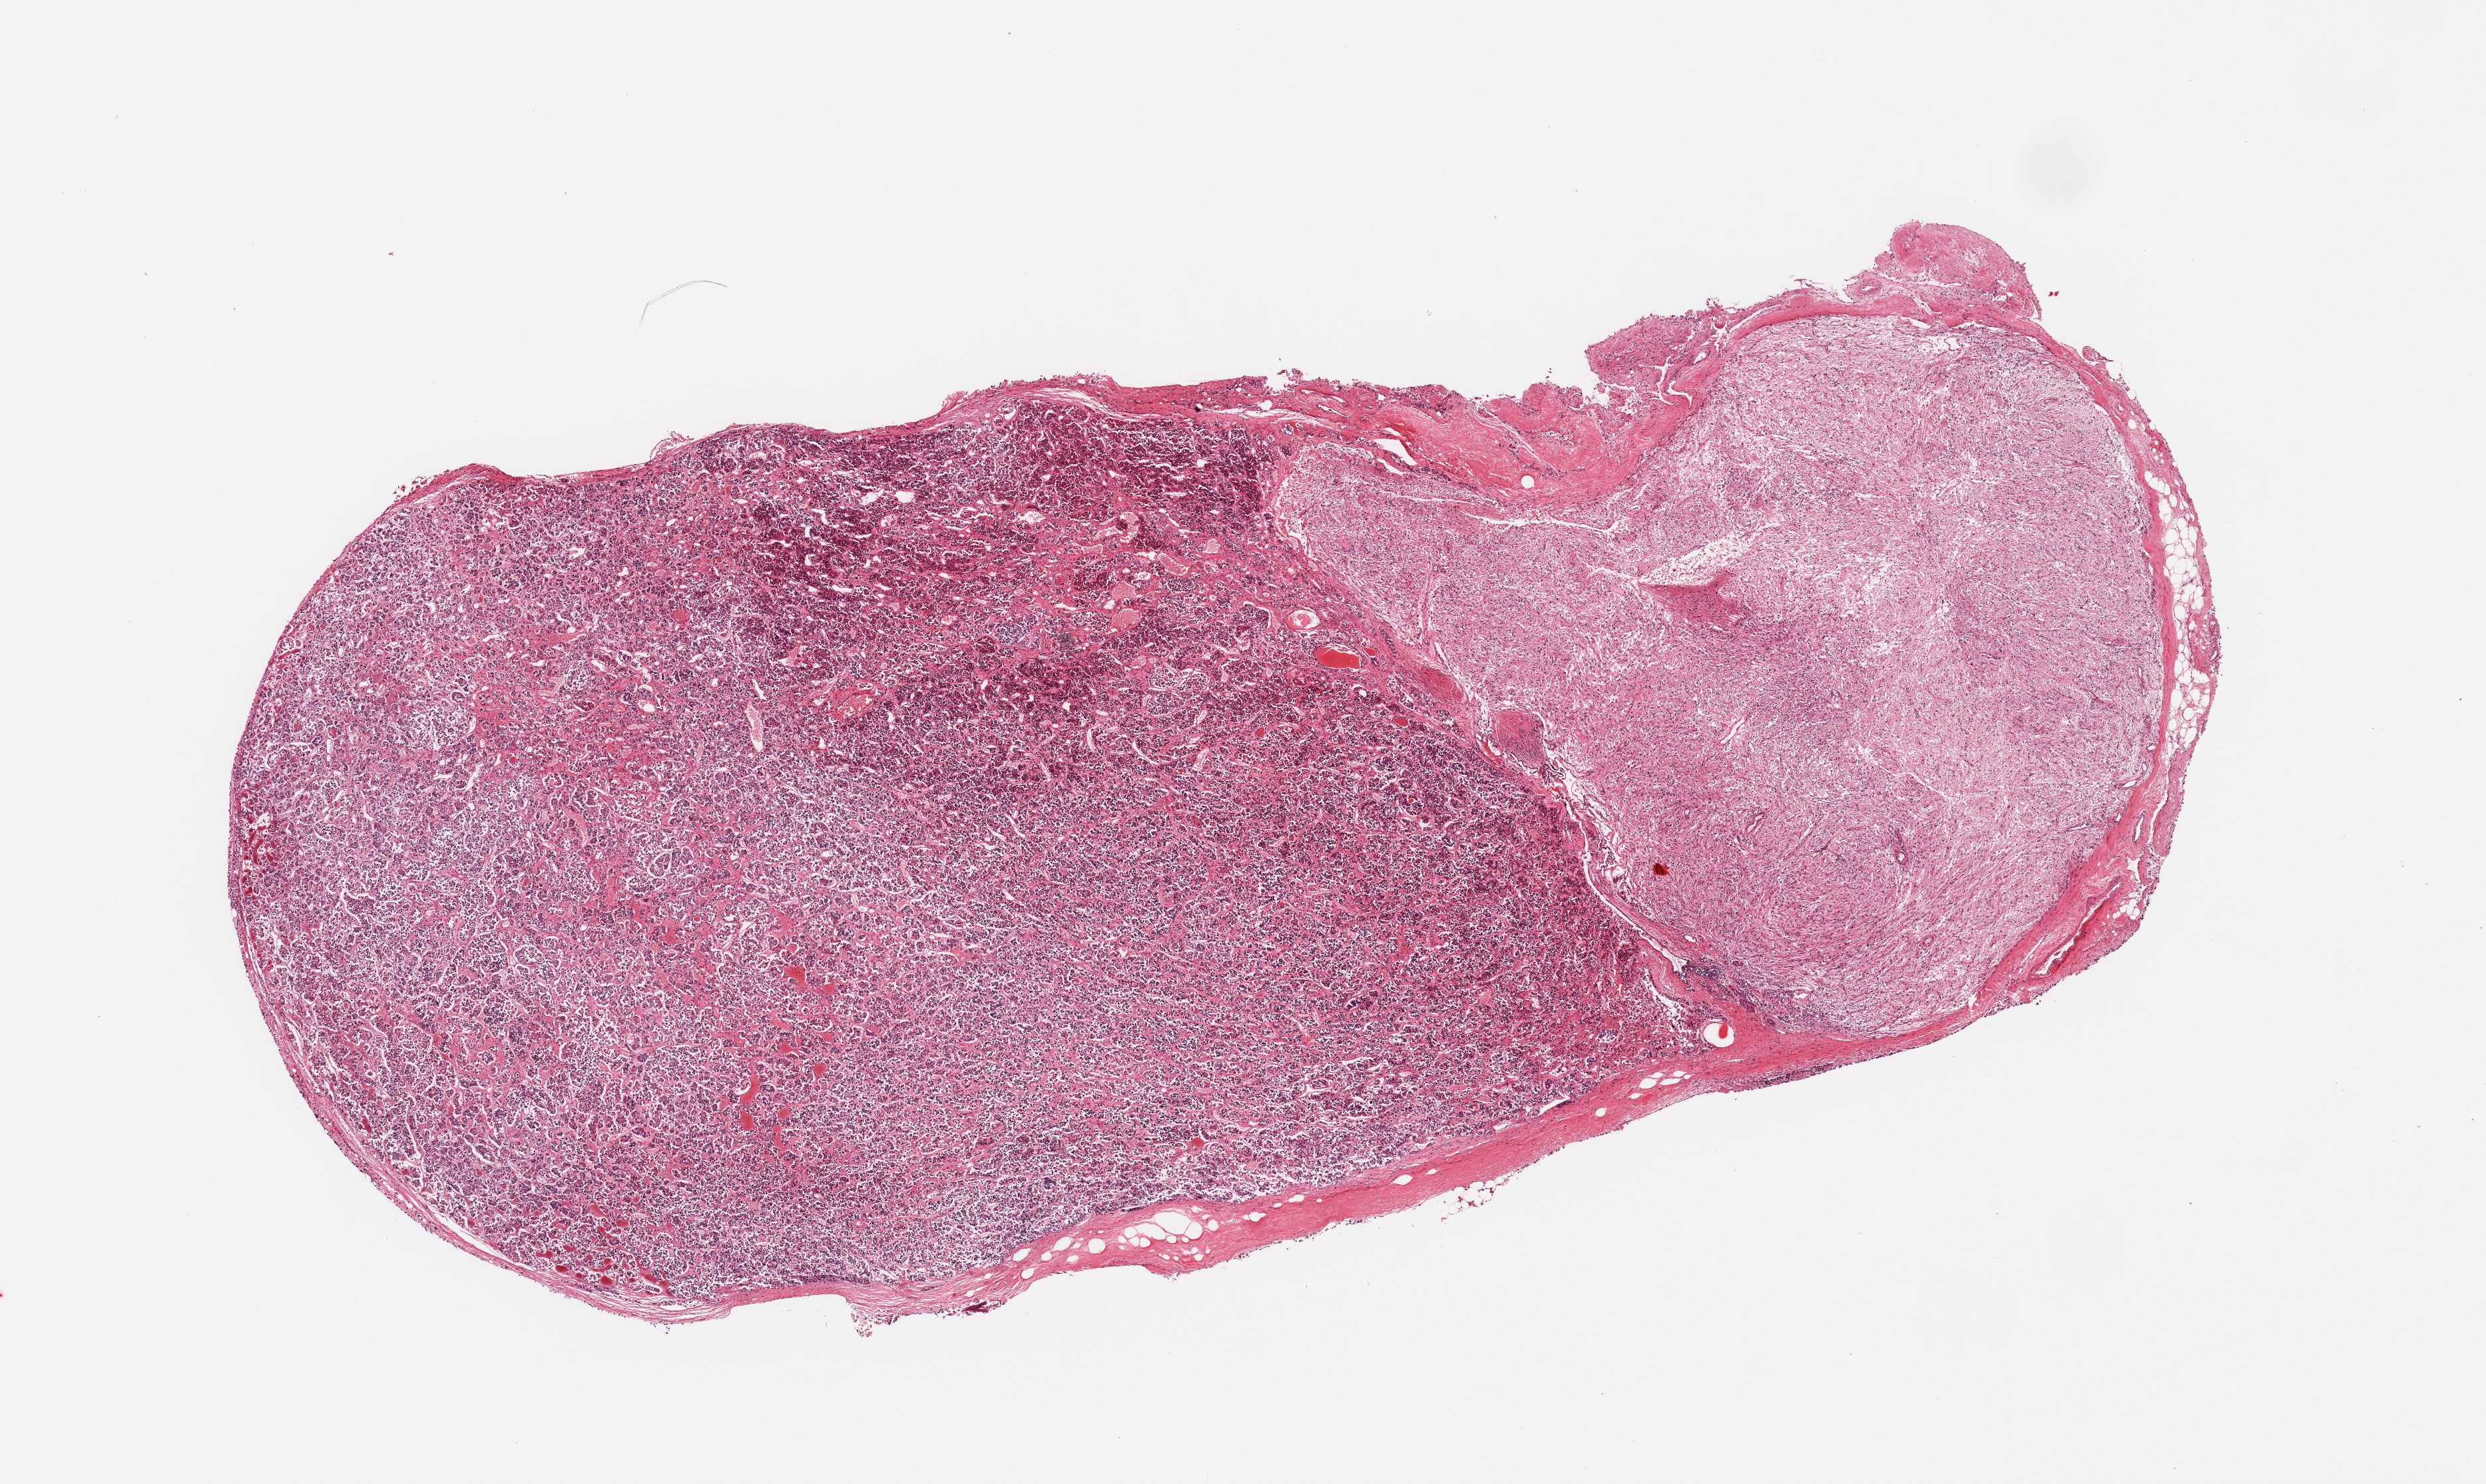
H&E whole-slide image, brightfield, whole scanned area (about 14.8 x 8.8 mm) shown as a low-resolution overview; PAXgene-fixed paraffin-embedded (PFPE) section; sampled site (target tissue): pituitary; donor tissue sample. Male donor.
• reviewer comment on this tissue sample: 1 piece; mildly to moderately autolyzed adenohypophysis and neurohypophysis